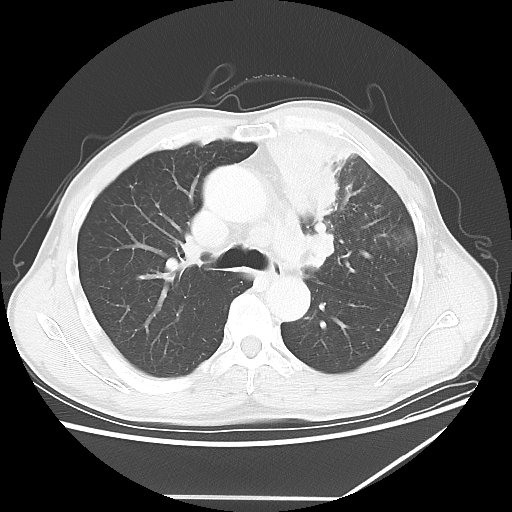
Chest CT, one axial slice; position 41 of 64 along the scan axis; lung window (W 1500 / L -600 HU); 512 × 512 image matrix, field of view 383 × 383 mm. Patient: male, 64 years. From the clinical record (not read from this slice): clinical TNM (as recorded): T1c N1 M1.
Structures marked on this image (rectangle marked by the reading radiologist):
- lung tumour (recorded histology: squamous cell carcinoma): bounding box (x1, y1, x2, y2) in pixels: (261, 127, 376, 238)